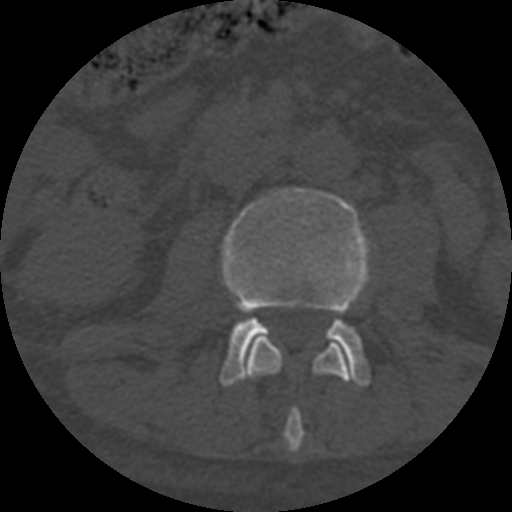
CT including the spine, one axial slice; position 244 of 708 along the scan axis; reconstruction kernel STANDARD; 120 kVp; one of 3 acquisitions stored at this slice position; bone window (W 1800 / L 400 HU); 512 × 512 image matrix, field of view 160 × 160 mm. Patient age 55 years. From the clinical record (not read from this slice): primary cancer: colon; vertebrae with lytic lesions (as recorded): T12, L1, L5.
Outlined on this slice (semi-automatic segmentation, software-assisted and operator-edited):
- L2 vertebra: bounding box (x1, y1, x2, y2) in pixels: (245, 337, 351, 453)
- L3 vertebra: (220, 188, 369, 386)